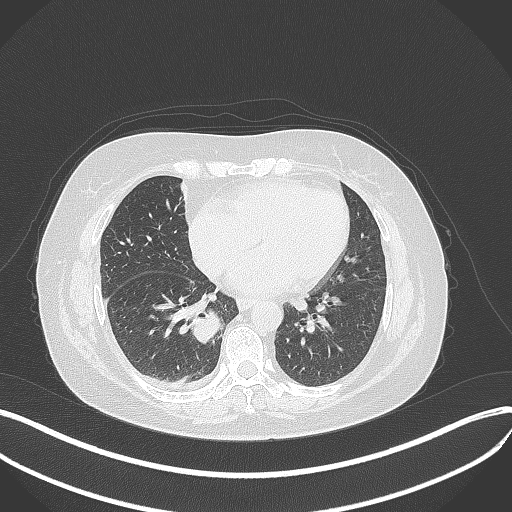
Chest CT, one axial slice; slice 141 of 381 in the series (ordered by position); 120 kVp; lung window (W 1500 / L -600 HU); 1 mm slice thickness; 512 × 512 image matrix, field of view 400 × 400 mm. Female patient, age 56 years. From the clinical record (not read from this slice): clinical TNM (as recorded): T2b N1 M0; histopathological grade: G3.
Annotated regions visible in this slice (bounding box drawn by a radiologist):
- lung tumour (recorded histology: small cell carcinoma): box from (x=191, y=308) to (x=226, y=348) px